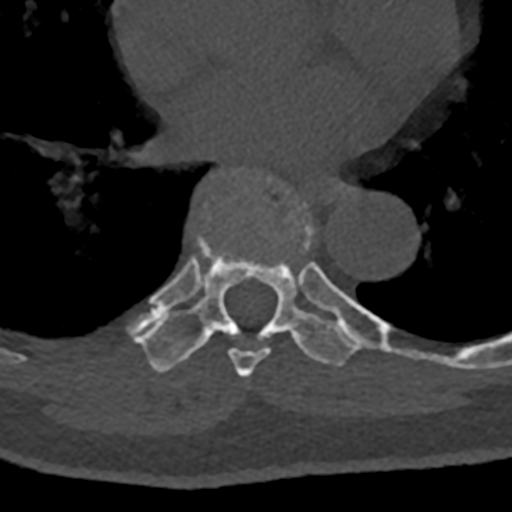
CT including the spine, one axial slice; slice 730 of 797 in the series (ordered by position); 120 kVp; bone window (W 1800 / L 400 HU); 512 × 512 image matrix. Male patient, age 74 years. From the clinical record (not read from this slice): primary cancer: renal.
Structures marked on this image (semi-automatically segmented with operator editing):
- T7 vertebra: bounding box [x1, y1, x2, y2] px = [208, 168, 354, 378]
- T8 vertebra: [132, 204, 430, 372]